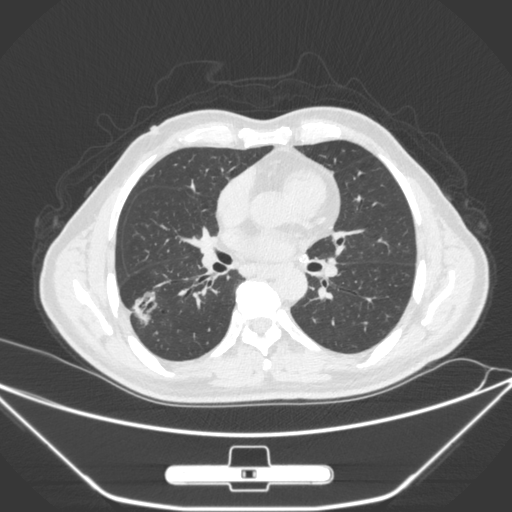
Chest CT, one axial slice. Slice 147 of 310 in the series (ordered by position). 120 kVp. Lung window (W 1500 / L -600 HU). 1 mm slice thickness. 512 × 512 image matrix, field of view 398 × 398 mm. Patient: male, 71 years. Case-level facts recorded for this patient, not image findings: clinical TNM (as recorded): T1c N0 M0; histopathological grade: G2.
Structures marked on this image (bounding box drawn by a radiologist):
- lung tumour (recorded histology: adenocarcinoma): bounding box (x1, y1, x2, y2) in pixels: (129, 283, 163, 329)